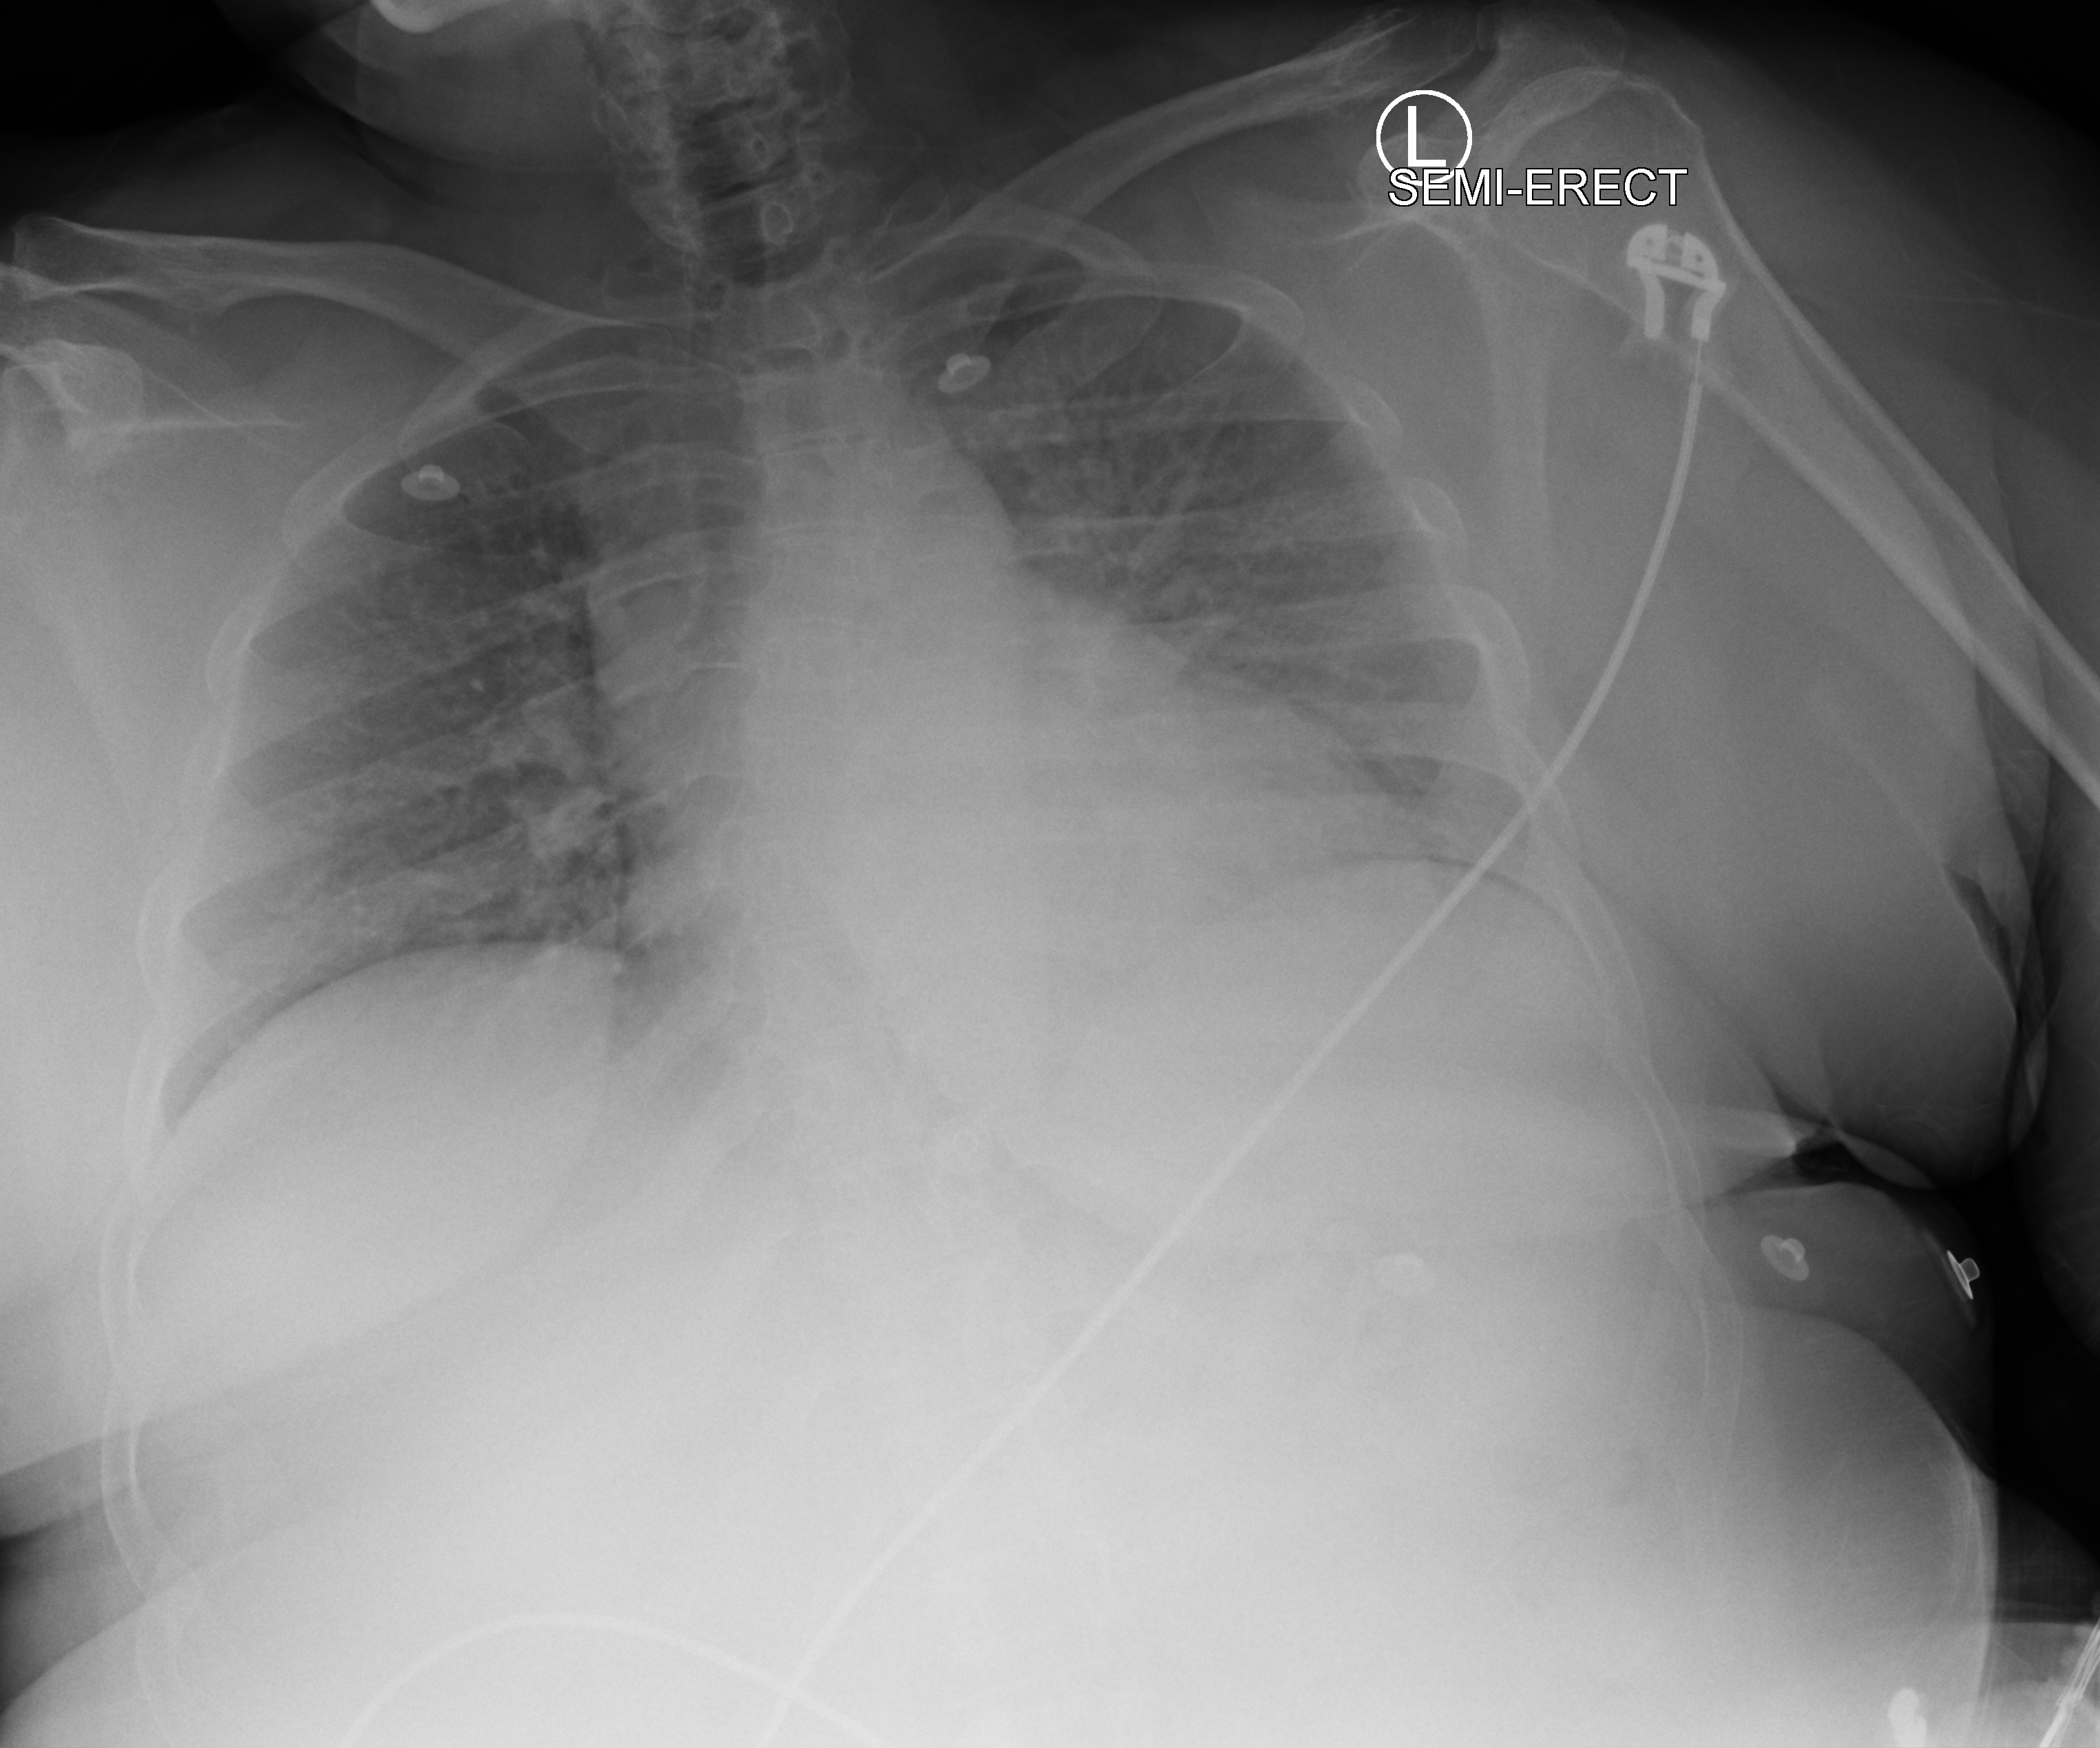
Bedside chest radiograph (computed radiography), anteroposterior (AP) projection. Patient hospitalised with COVID-19; female, aged 18–59 years.
From the hospital-stay record, not from the radiograph (when in the stay this image was taken is not recorded):
- mechanically ventilated during this hospital stay: no
- hypertension (admission record): yes
- diabetes (admission record): no